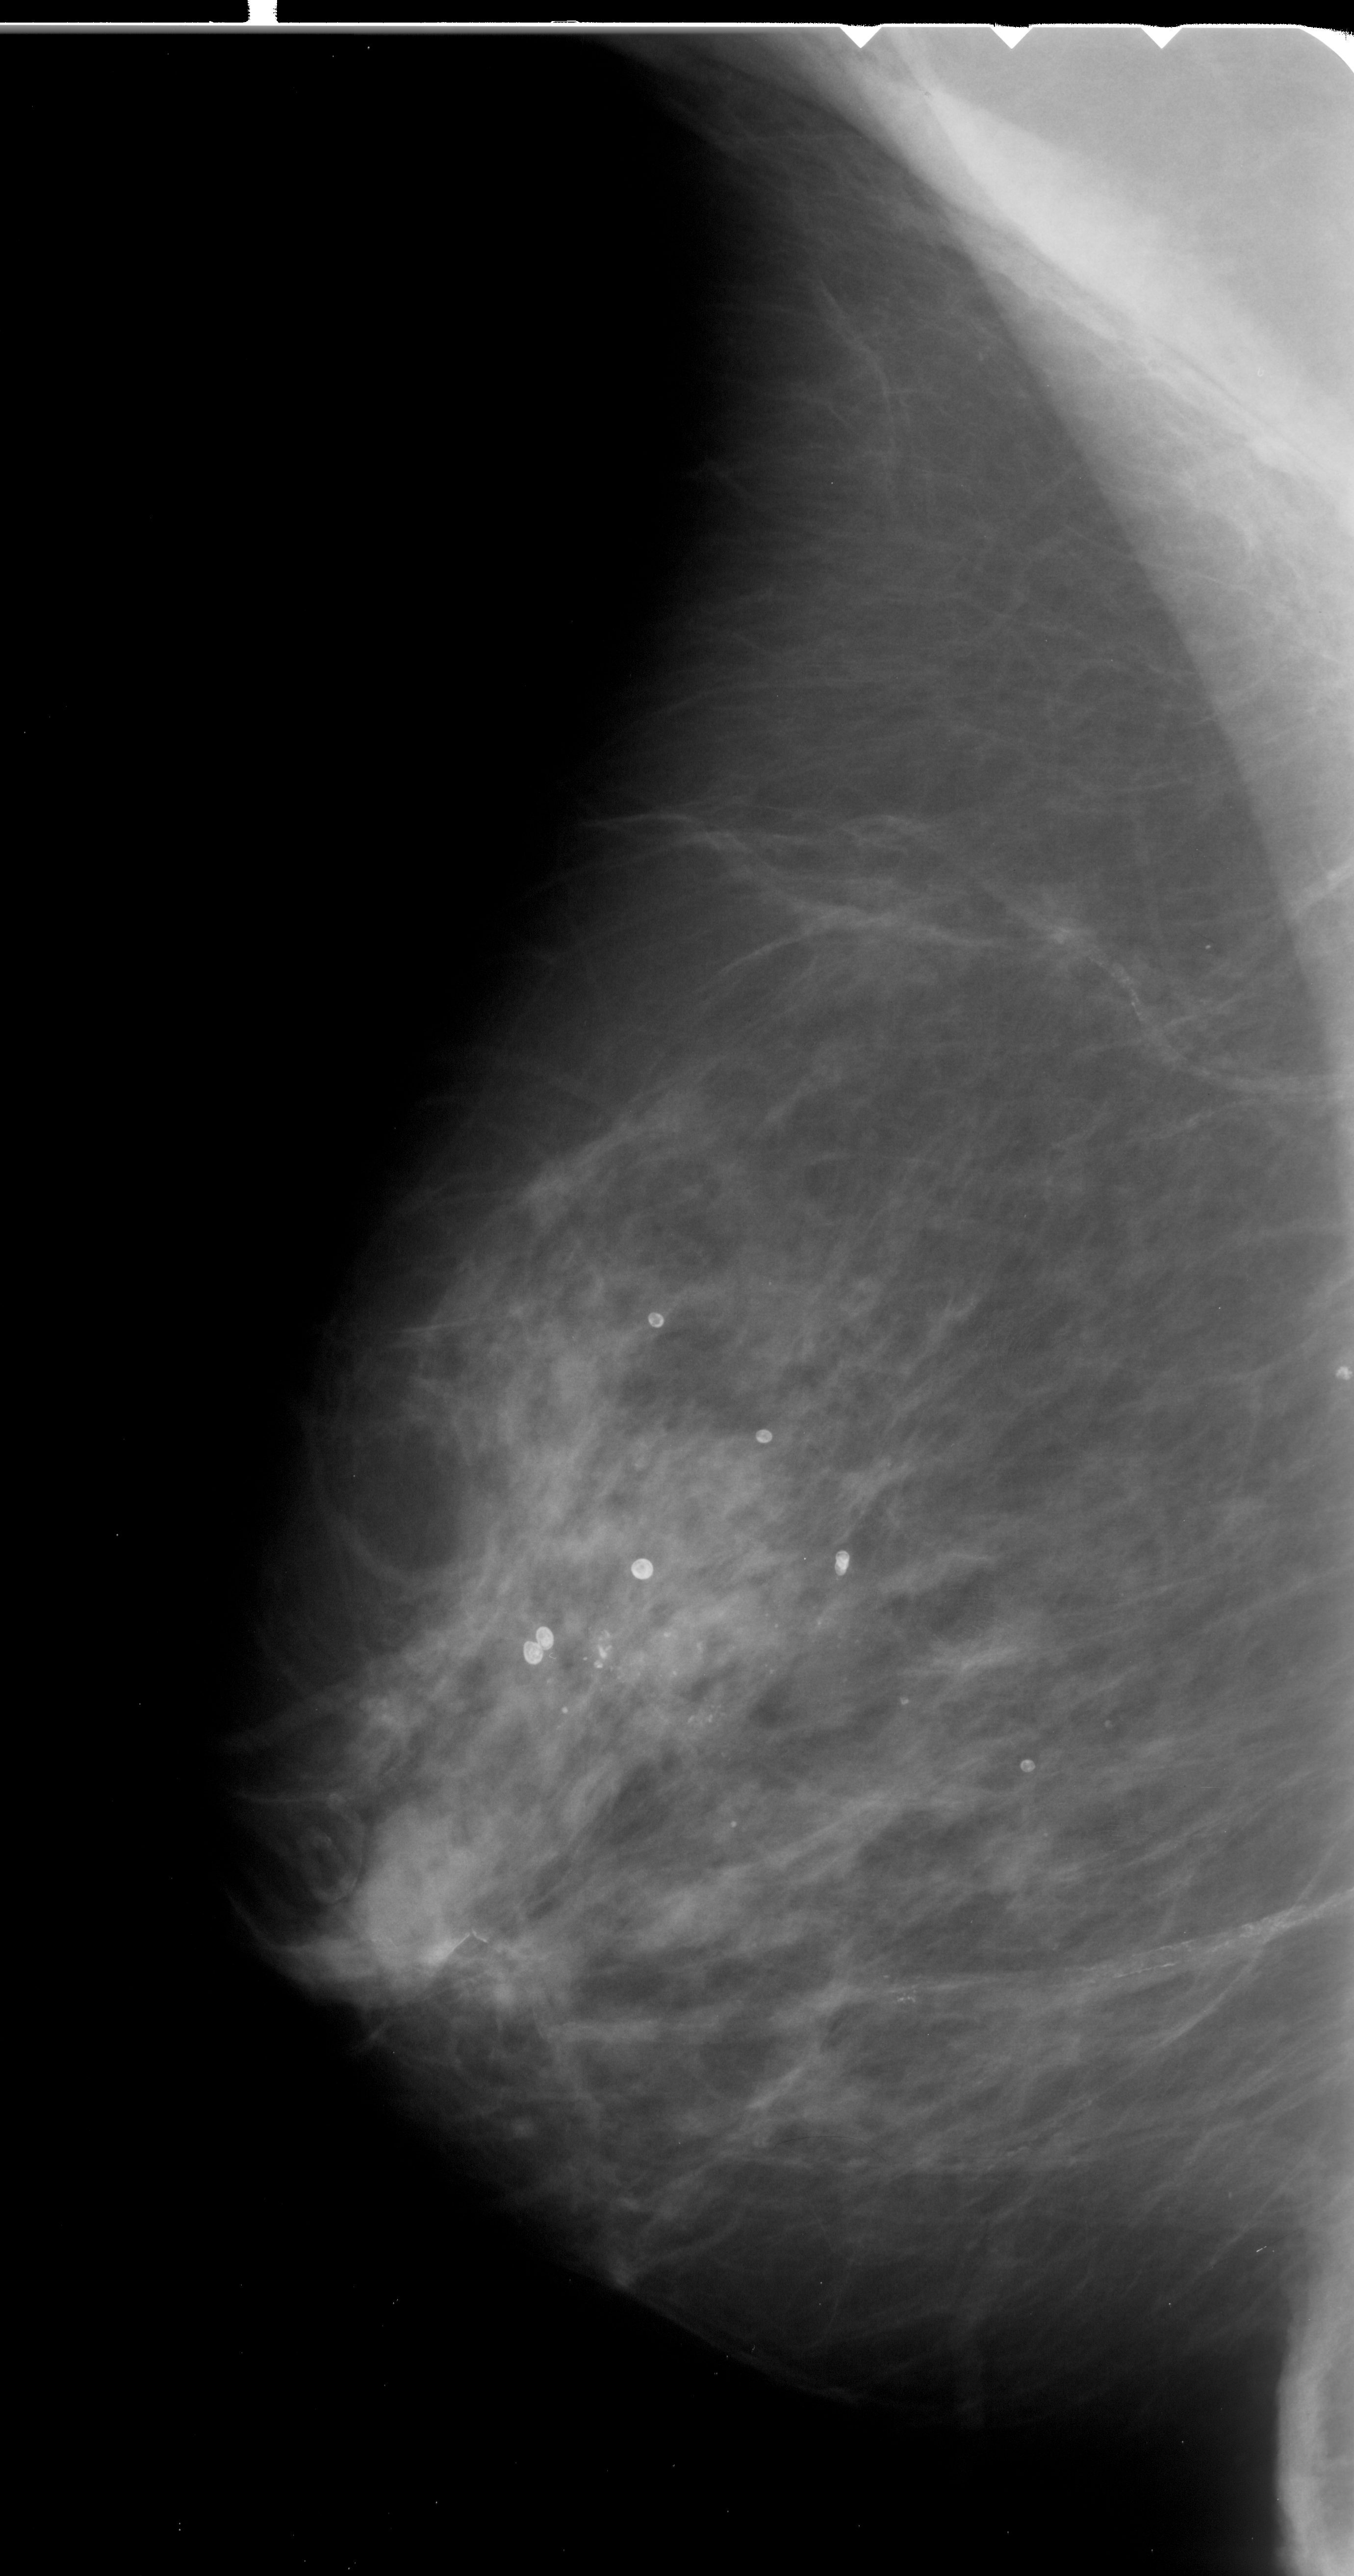
Scanned film-screen mammogram; left breast; mediolateral oblique (MLO) view; 1354 × 2576 image matrix.
Marked abnormalities (boxes around the expert regions of interest):
- calcifications, morphology pleomorphic, distribution segmental; BI-RADS assessment category 4; subtlety rating 3 on a 1 (subtle) to 5 (obvious) scale; pathology result (as recorded, not read from the image): malignant: box from (x=496, y=1563) to (x=904, y=1788) px